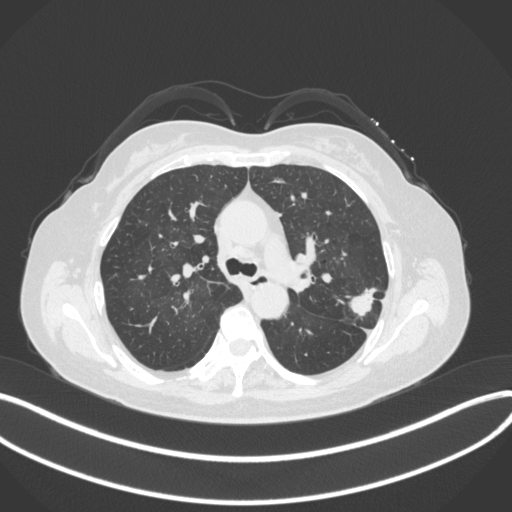
Chest CT, one axial slice; position 224 of 330 along the scan axis; reconstruction kernel B31f; 120 kVp; lung window (W 1500 / L -600 HU); 1 mm slice thickness; 512 × 512 image matrix. Female patient, age 60 years. Case-level facts recorded for this patient, not image findings: clinical TNM (as recorded): T1c N0 M0.
Annotated regions visible in this slice (rectangle marked by the reading radiologist):
- lung tumour (recorded histology: adenocarcinoma): bounding box (x1, y1, x2, y2) in pixels: (345, 285, 382, 320)